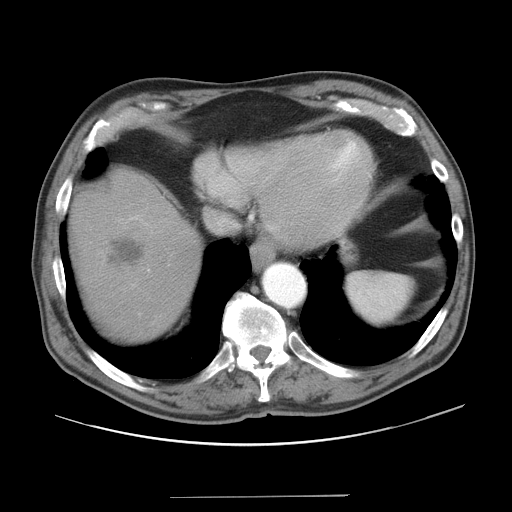
Contrast-enhanced abdominal CT, one axial slice; slice 36 of 41 in the series (ordered by position); intravenous contrast given; soft-tissue window (W 400 / L 40 HU); 5 mm slice thickness; 512 × 512 image matrix, field of view 420 × 420 mm. Male patient, age 75 years. From the clinical record (not read from this slice): diagnosis: colorectal cancer liver metastases, imaged before liver resection.
Outlined on this slice (outlined manually by an expert reader):
- hepatic veins: box from (x=208, y=216) to (x=236, y=231) px
- liver: (x=73, y=174)–(x=200, y=338)
- planned liver remnant (the part of the liver to remain after resection): (x=107, y=232)–(x=200, y=338)
- portal vein (with intrahepatic branches): (x=147, y=269)–(x=150, y=272)
- liver metastasis: (x=108, y=237)–(x=144, y=267)